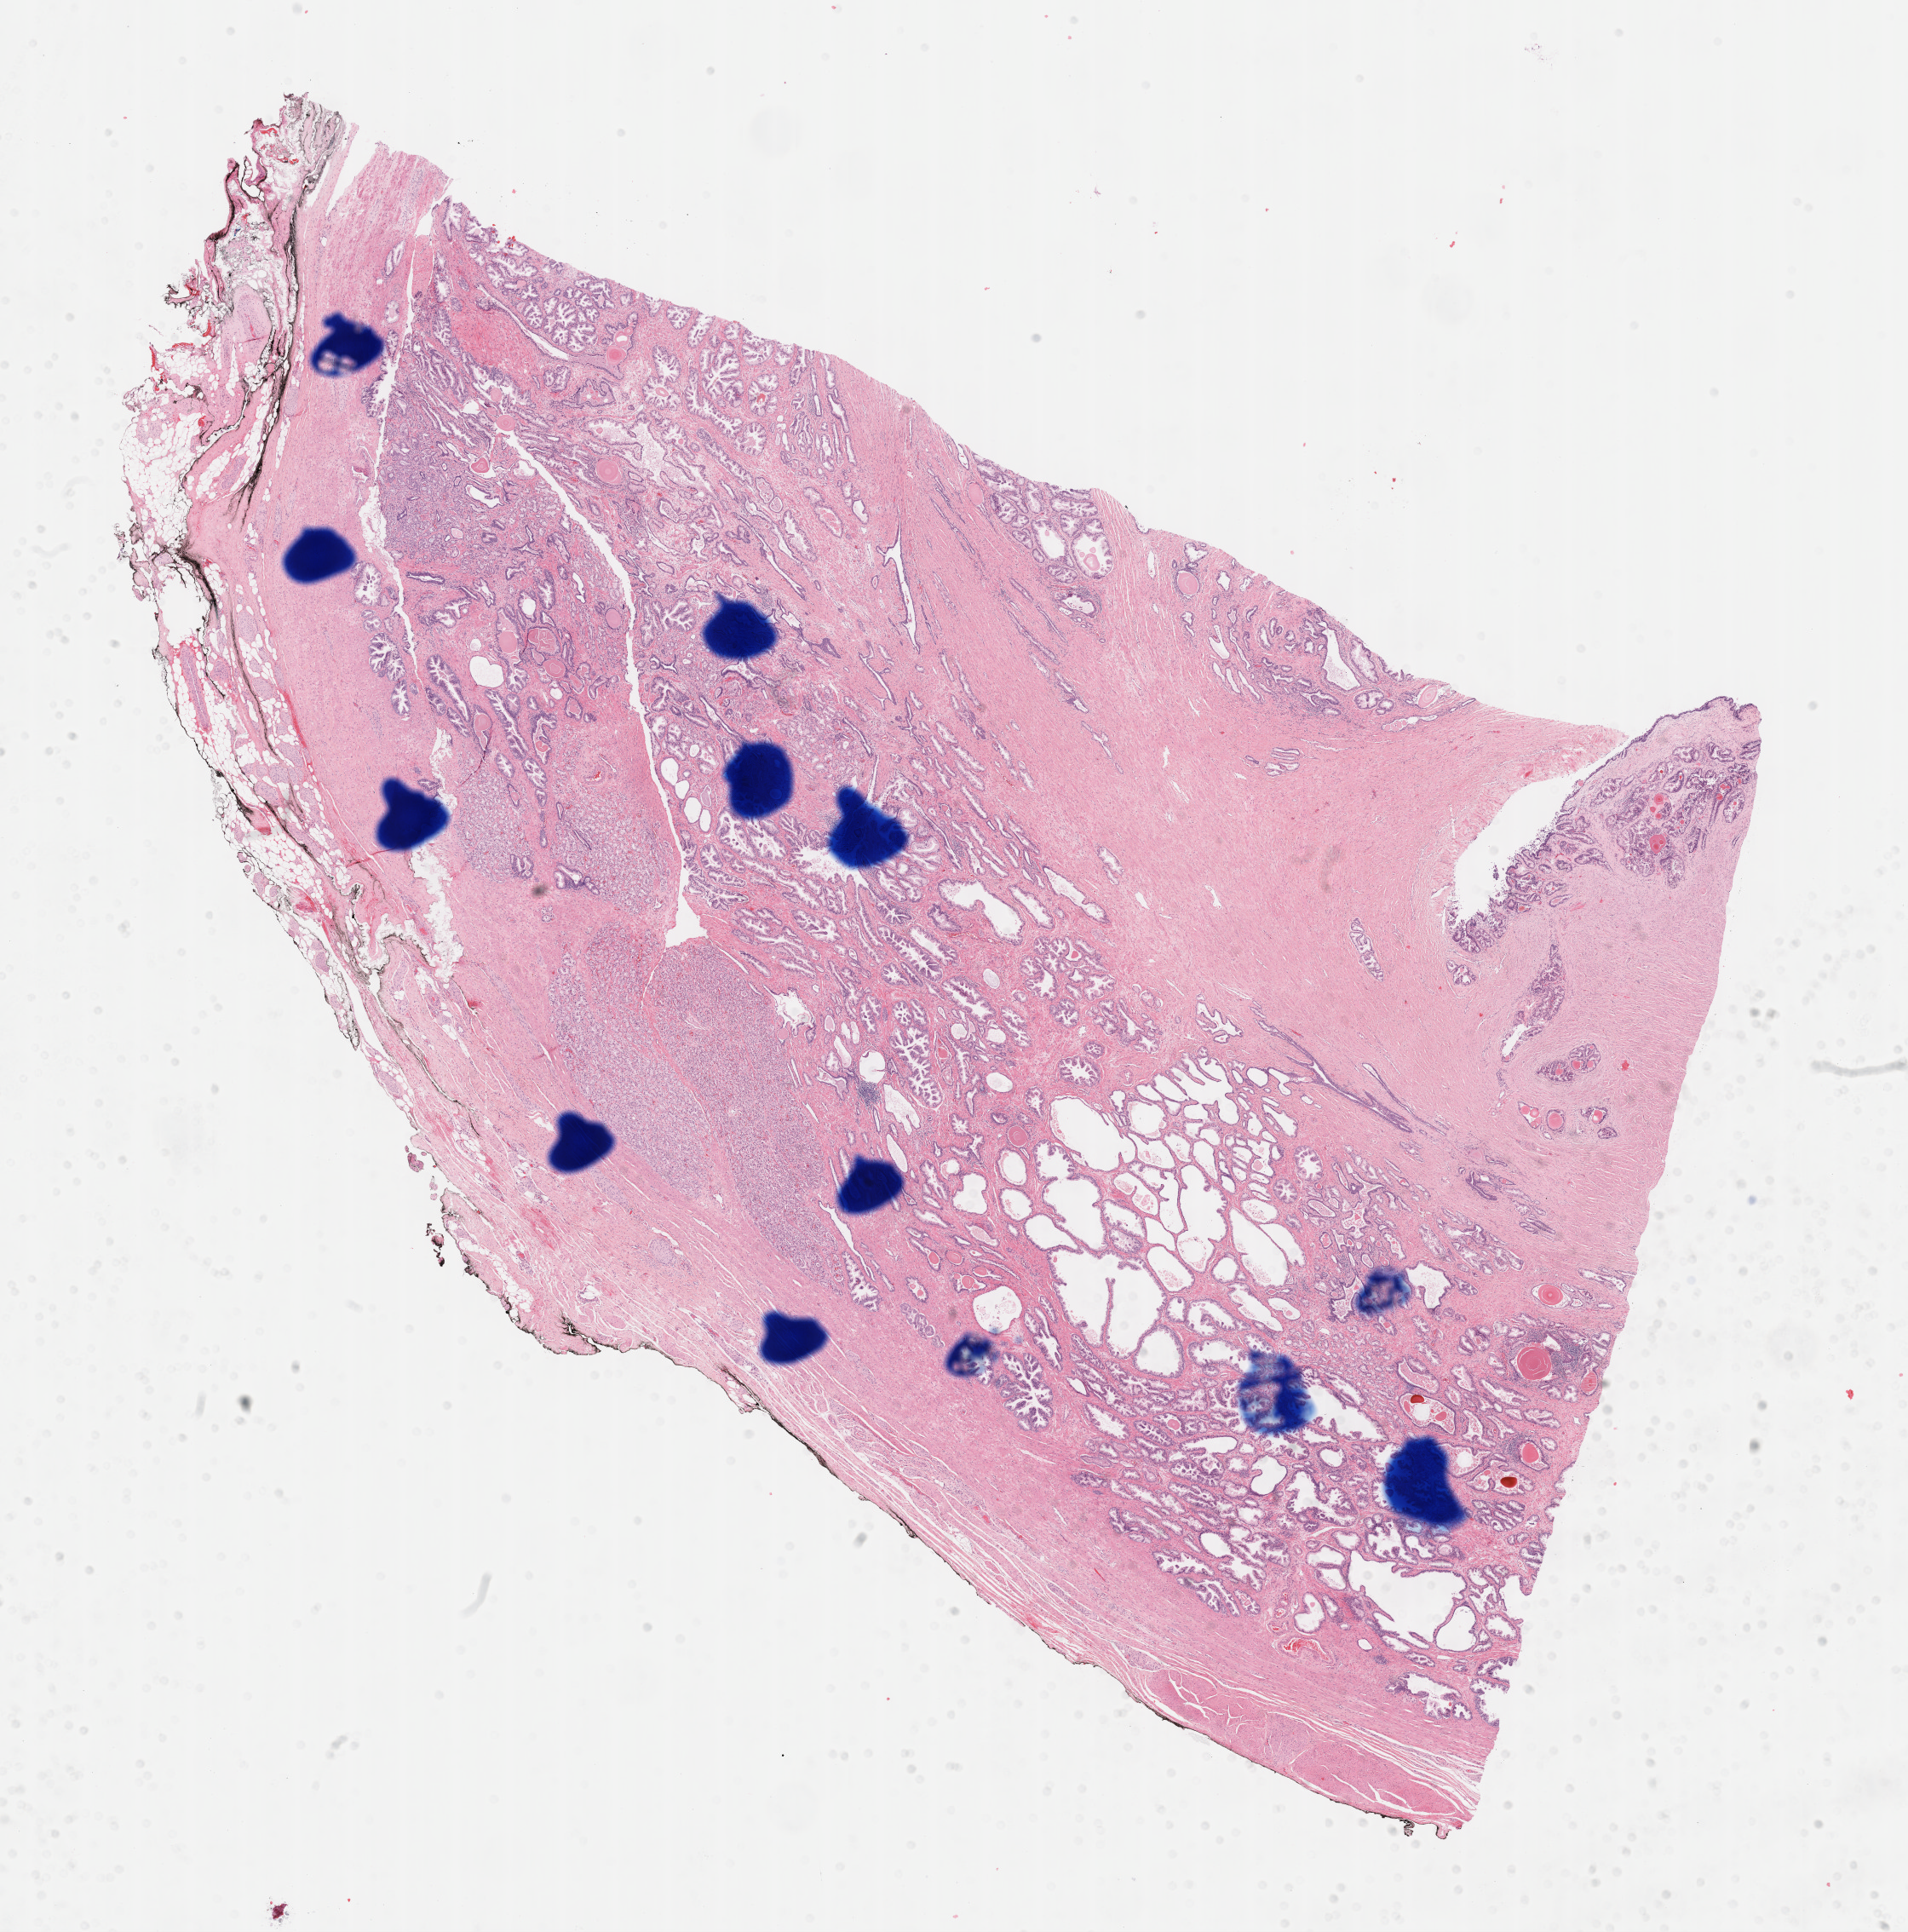
H&E whole-slide image, low-resolution overview of the scanned area, about 18.1 x 18.3 mm (from a 40x scan), FFPE section, sample: primary tumour, prostate. Patient: male, age at initial diagnosis 63 years.
Pathologic diagnosis: Adenocarcinoma, NOS (prostate gland).